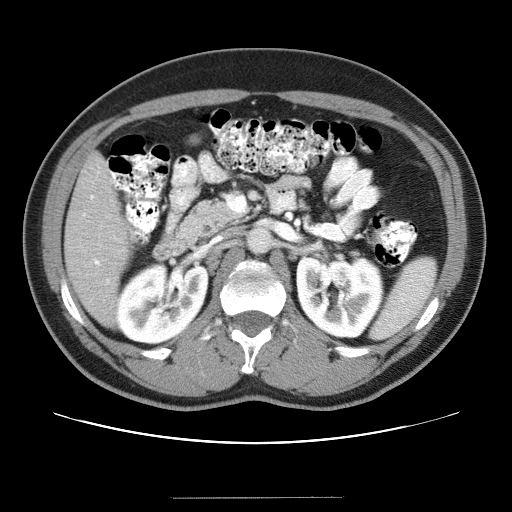
Contrast-enhanced abdominal CT (liver protocol), one axial slice. Slice 11 of 40 in the series (ordered by position). 120 kVp. Soft-tissue window (W 400 / L 40 HU). 5 mm slice thickness. 512 × 512 image matrix, field of view 380 × 380 mm. Case-level facts recorded for this patient, not image findings: diagnosis: hepatocellular carcinoma (patient treated with transarterial chemoembolisation; whether this scan precedes or follows treatment is not stated here); TNM stage (as recorded): Stage-IVA; Child-Pugh class: B; tumour nodularity: multinodular.
Annotated regions visible in this slice (semi-automatic segmentation, software-assisted and operator-edited):
- liver parenchyma outside the tumour (the mass and vessels are separate outlines, so this box may not span the whole liver): bounding box <64,152,131,324> (left, top, right, bottom; pixels)
- liver vessels: <83,172,117,284>